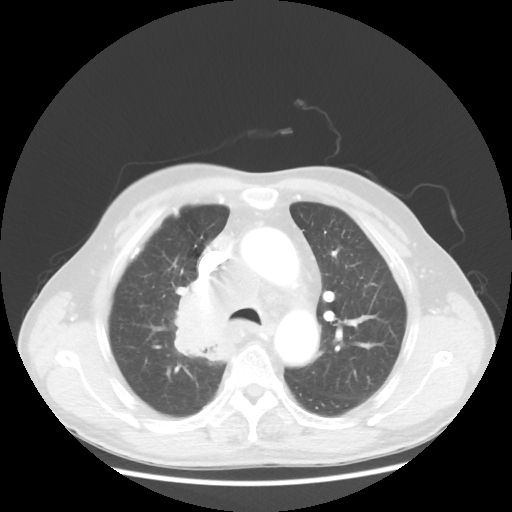
Chest CT, one axial slice; reconstruction kernel STANDARD; 100 kVp; lung window (W 1500 / L -600 HU); 512 × 512 image matrix. Male patient, age 64 years. Case-level facts recorded for this patient, not image findings: clinical TNM (as recorded): T3 N3 M0; histopathological grade: G3.
Annotated regions visible in this slice (bounding box drawn by a radiologist):
- lung tumour (recorded histology: small cell carcinoma): bounding box [x1, y1, x2, y2] px = [145, 273, 249, 372]